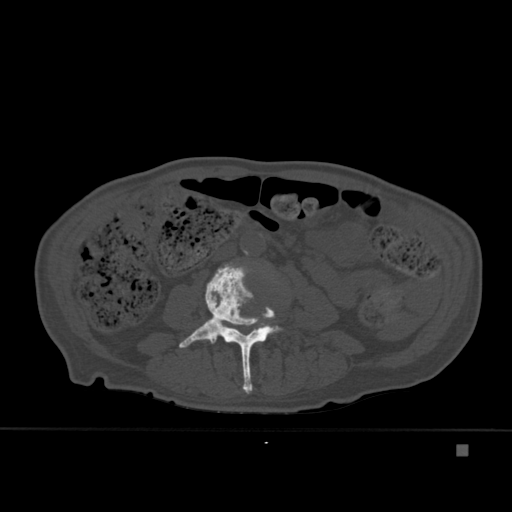
CT including the spine, one axial slice. Bone window (W 1800 / L 400 HU). 1.5 mm slice thickness. 512 × 512 image matrix, field of view 378 × 378 mm. Male patient, age 75 years. From the clinical record (not read from this slice): primary cancer: prostate.
Outlined on this slice (semi-automatically segmented with operator editing):
- L3 vertebra: bounding box (x1, y1, x2, y2) in pixels: (179, 262, 282, 394)
- L4 vertebra: (252, 322, 279, 334)